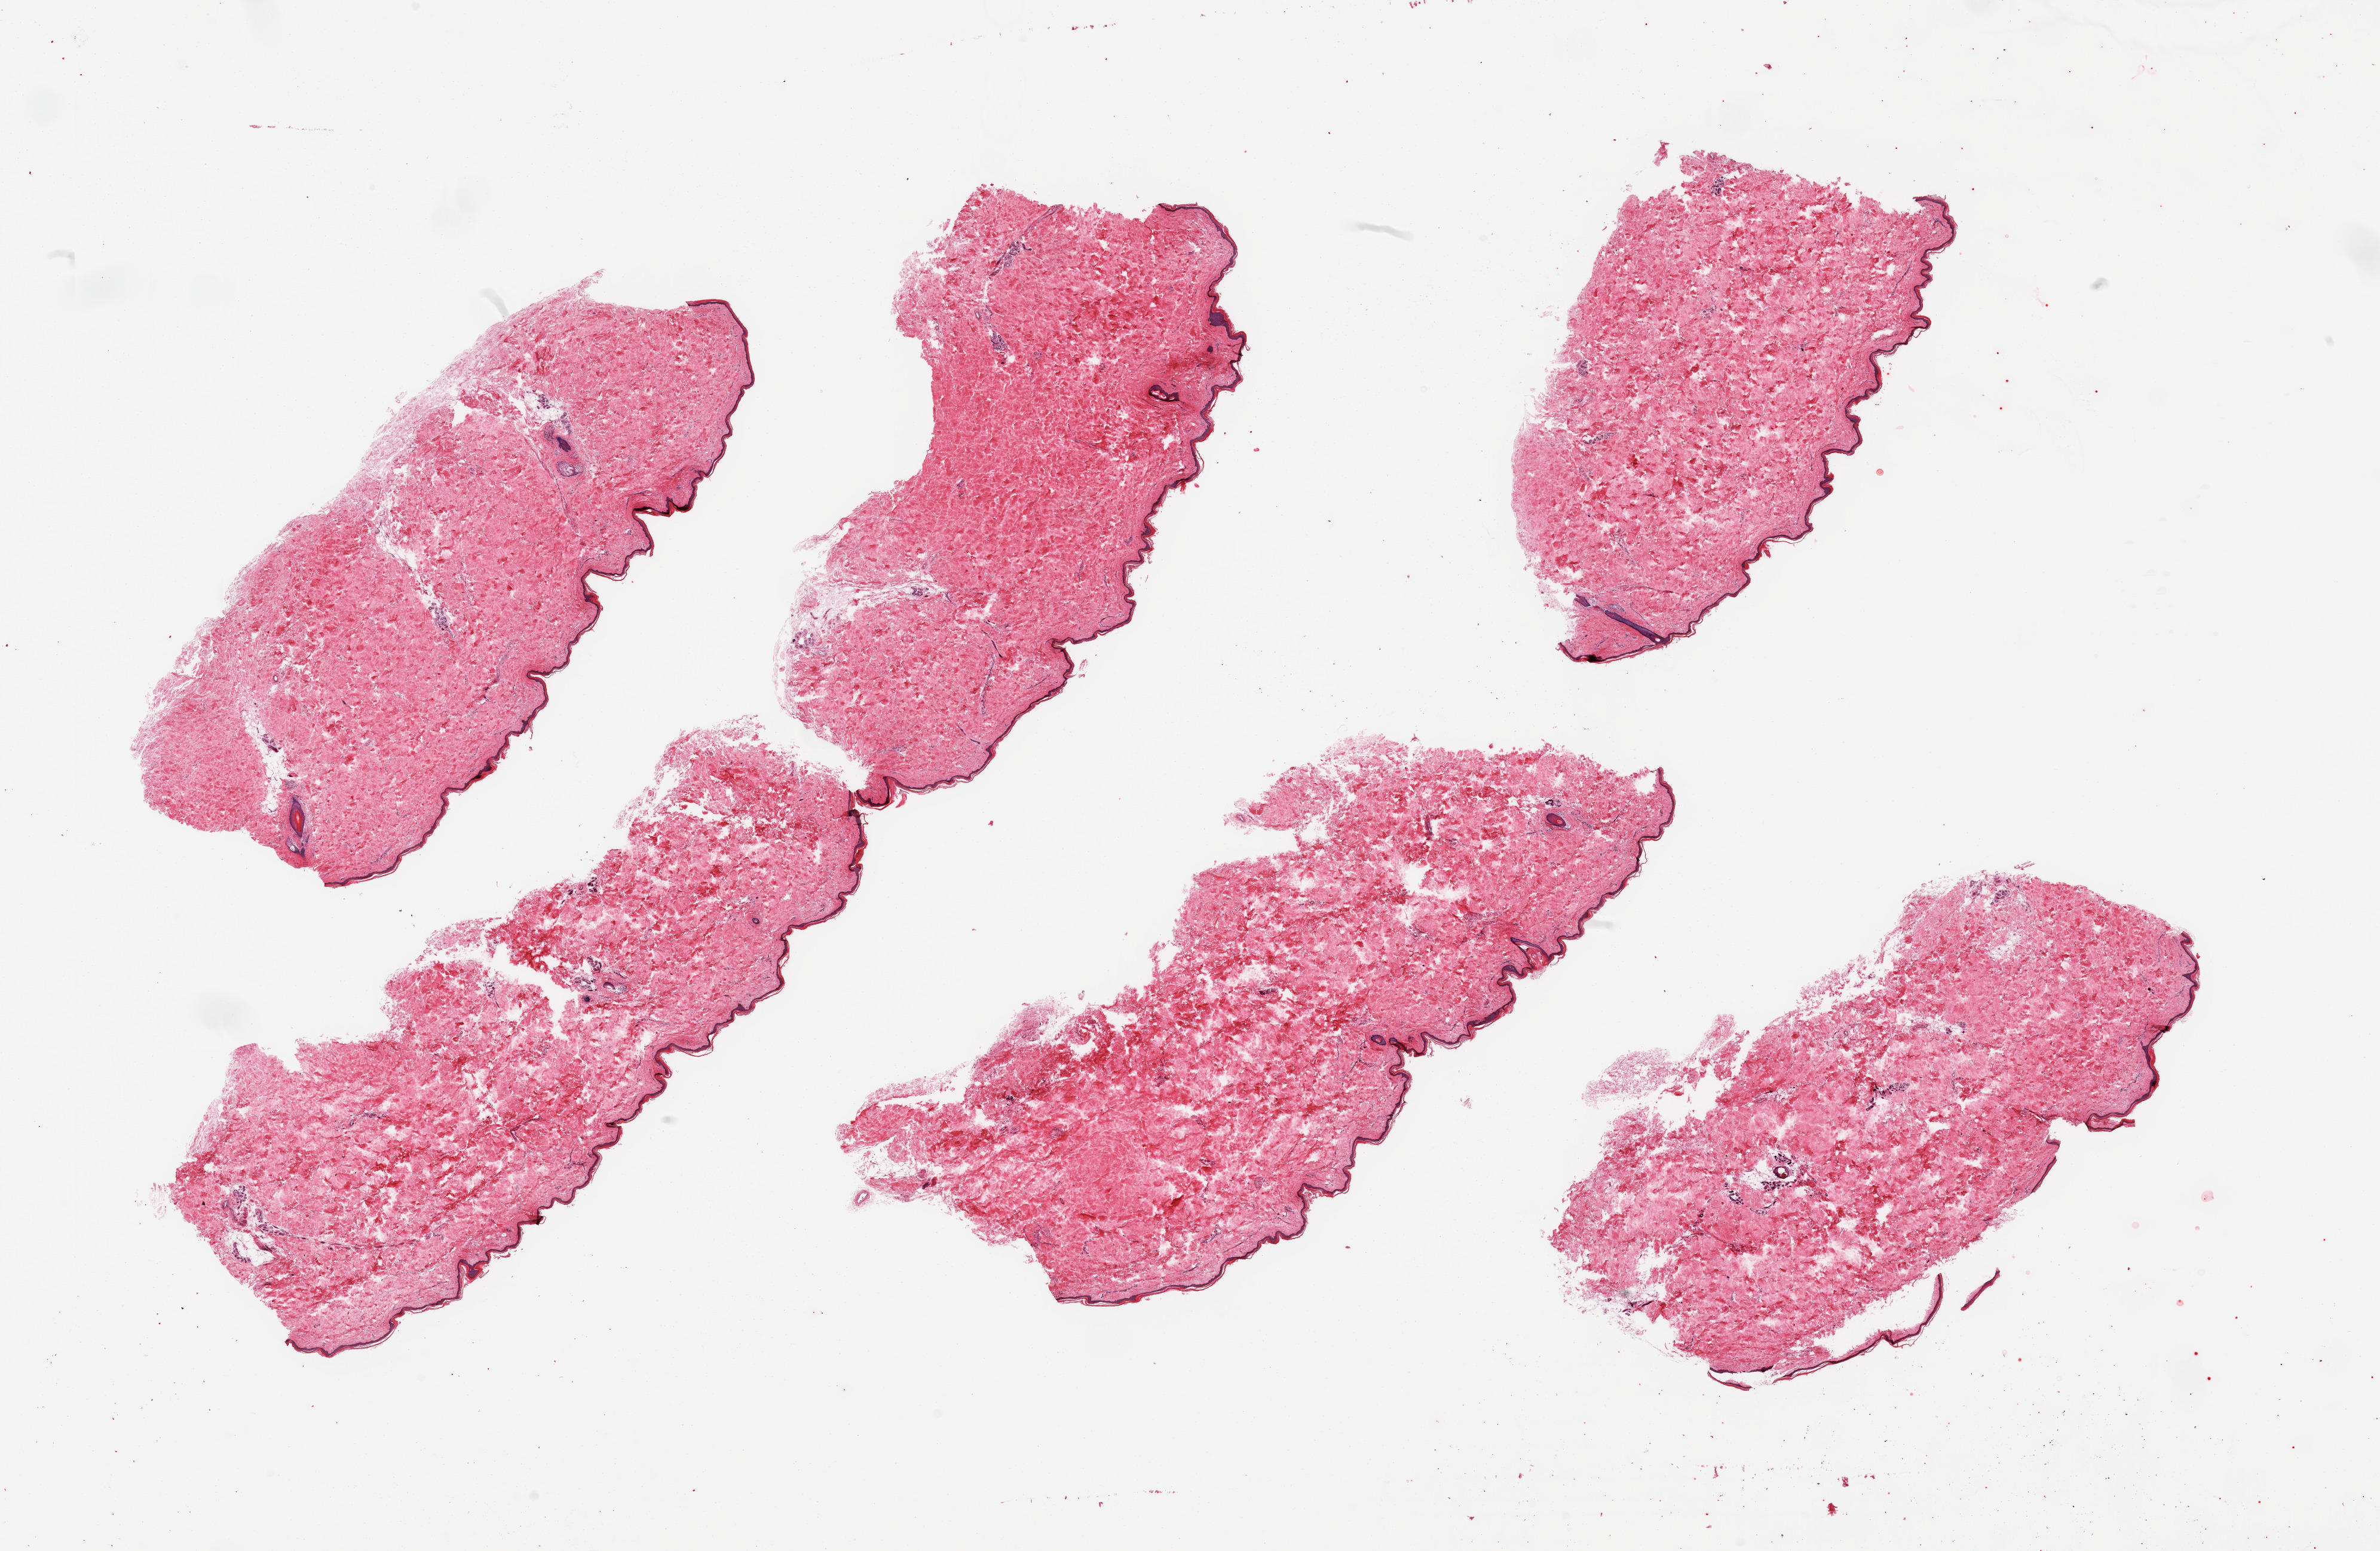
H&E whole-slide image, brightfield — whole scanned area (about 31.5 x 20.5 mm) shown as a low-resolution overview, PAXgene-fixed paraffin-embedded (PFPE) section, section of skin of lower leg (target tissue), tissue donor sample.
* review note (as recorded): 6 pieces; well trimmed, epidermis measures 29 microns